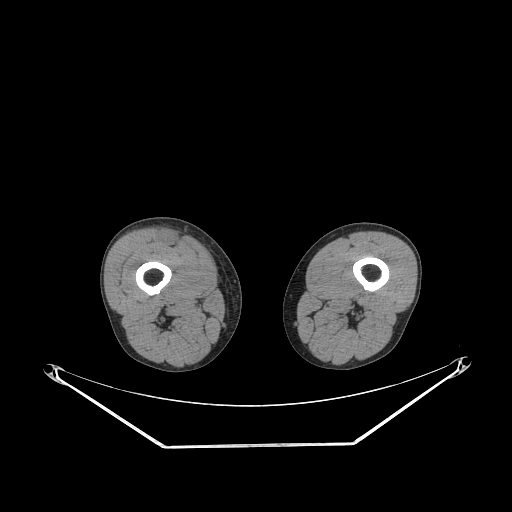
CT of an extremity soft-tissue mass (from a PET/CT study), one axial slice. Position 227 of 311 along the scan axis. Reconstruction kernel STANDARD. Soft-tissue window (W 400 / L 40 HU). 512 × 512 image matrix. Male patient. Case-level facts recorded for this patient, not image findings: histological type: pleiomorphic leiomyosarcoma; grade: intermediate; site of the primary tumour: right thigh.
Annotated regions visible in this slice (expert contour drawn on MRI and transferred to this co-registered scan by the dataset authors):
- gross tumour volume including surrounding oedema: bounding box <160,233,182,247> (left, top, right, bottom; pixels)